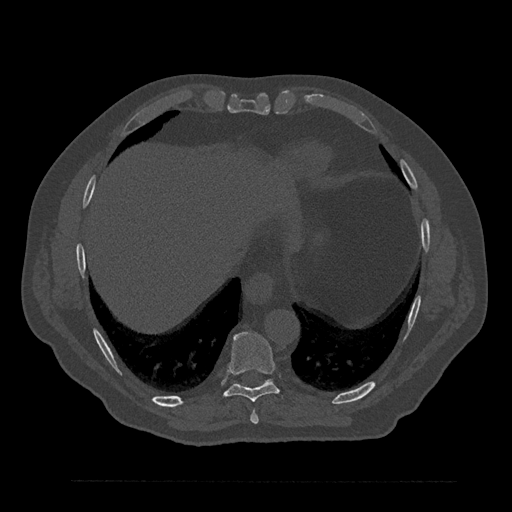
CT including the spine, one axial slice. Slice 399 of 797 in the series (ordered by position). 120 kVp. Bone window (W 1800 / L 400 HU). 512 × 512 image matrix, field of view 430 × 430 mm. Patient: male, 61 years. From the clinical record (not read from this slice): primary cancer: prostate.
Structures marked on this image (semi-automatically segmented with operator editing):
- T8 vertebra: bounding box (x1, y1, x2, y2) in pixels: (250, 410, 259, 424)
- T9 vertebra: (223, 332, 280, 402)